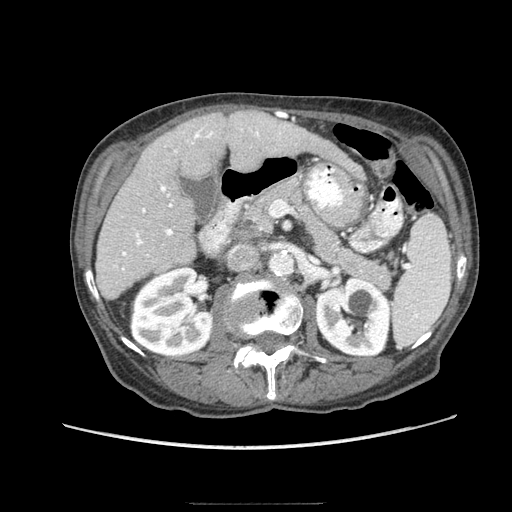
Contrast-enhanced abdominal CT (liver protocol), one axial slice; position 37 of 83 along the scan axis; reconstruction kernel STANDARD; soft-tissue window (W 400 / L 40 HU); 2.5 mm slice thickness; 512 × 512 image matrix, field of view 360 × 360 mm. Case-level facts recorded for this patient, not image findings: diagnosis: hepatocellular carcinoma (patient treated with transarterial chemoembolisation; whether this scan precedes or follows treatment is not stated here); TNM stage (as recorded): Stage-I; Child-Pugh class: A.
Outlined on this slice (semi-automatically segmented with operator editing):
- liver parenchyma outside the tumour (the mass and vessels are separate outlines, so this box may not span the whole liver): bounding box <96,110,336,298> (left, top, right, bottom; pixels)
- liver vessels: <114,127,285,271>